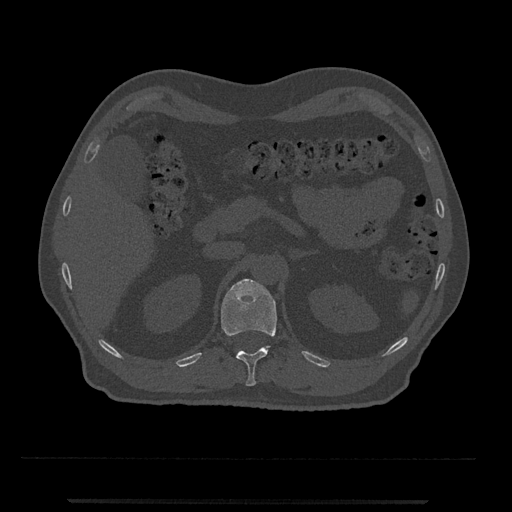
CT including the spine, one axial slice. Position 389 of 797 along the scan axis. Reconstruction kernel Br40s/3. 120 kVp. Bone window (W 1800 / L 400 HU). 0.5 mm slice thickness. 512 × 512 image matrix, field of view 419 × 419 mm. Male patient, age 63 years. Case-level facts recorded for this patient, not image findings: primary cancer: prostate.
Structures marked on this image (semi-automatic segmentation, software-assisted and operator-edited):
- T12 vertebra: box from (x=221, y=279) to (x=277, y=386) px